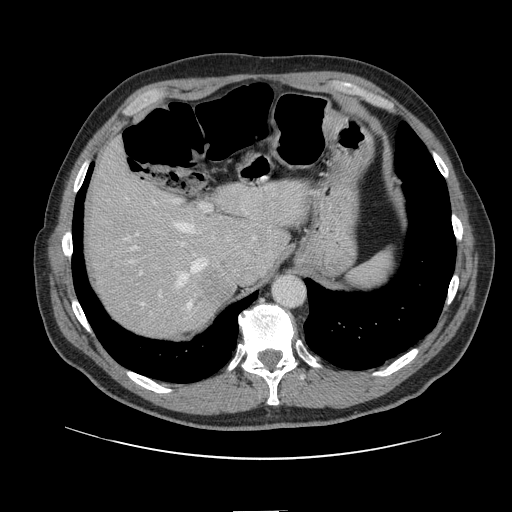
Contrast-enhanced abdominal CT, one axial slice. Position 107 of 161 along the scan axis. 120 kVp. Soft-tissue window (W 400 / L 40 HU). 2.5 mm slice thickness. 512 × 512 image matrix, field of view 412 × 412 mm. Male patient, age 66 years. Case-level facts recorded for this patient, not image findings: diagnosis: colorectal cancer liver metastases, imaged before liver resection; multiple liver metastases: no; largest metastasis: 3.5 cm.
Annotated regions visible in this slice (manually delineated by an expert):
- hepatic veins: box from (x=125, y=221) to (x=209, y=312) px
- liver: (x=89, y=146)–(x=307, y=337)
- planned liver remnant (the part of the liver to remain after resection): (x=89, y=145)–(x=307, y=307)
- portal vein (with intrahepatic branches): (x=128, y=200)–(x=212, y=298)
- liver metastasis: (x=199, y=267)–(x=233, y=307)